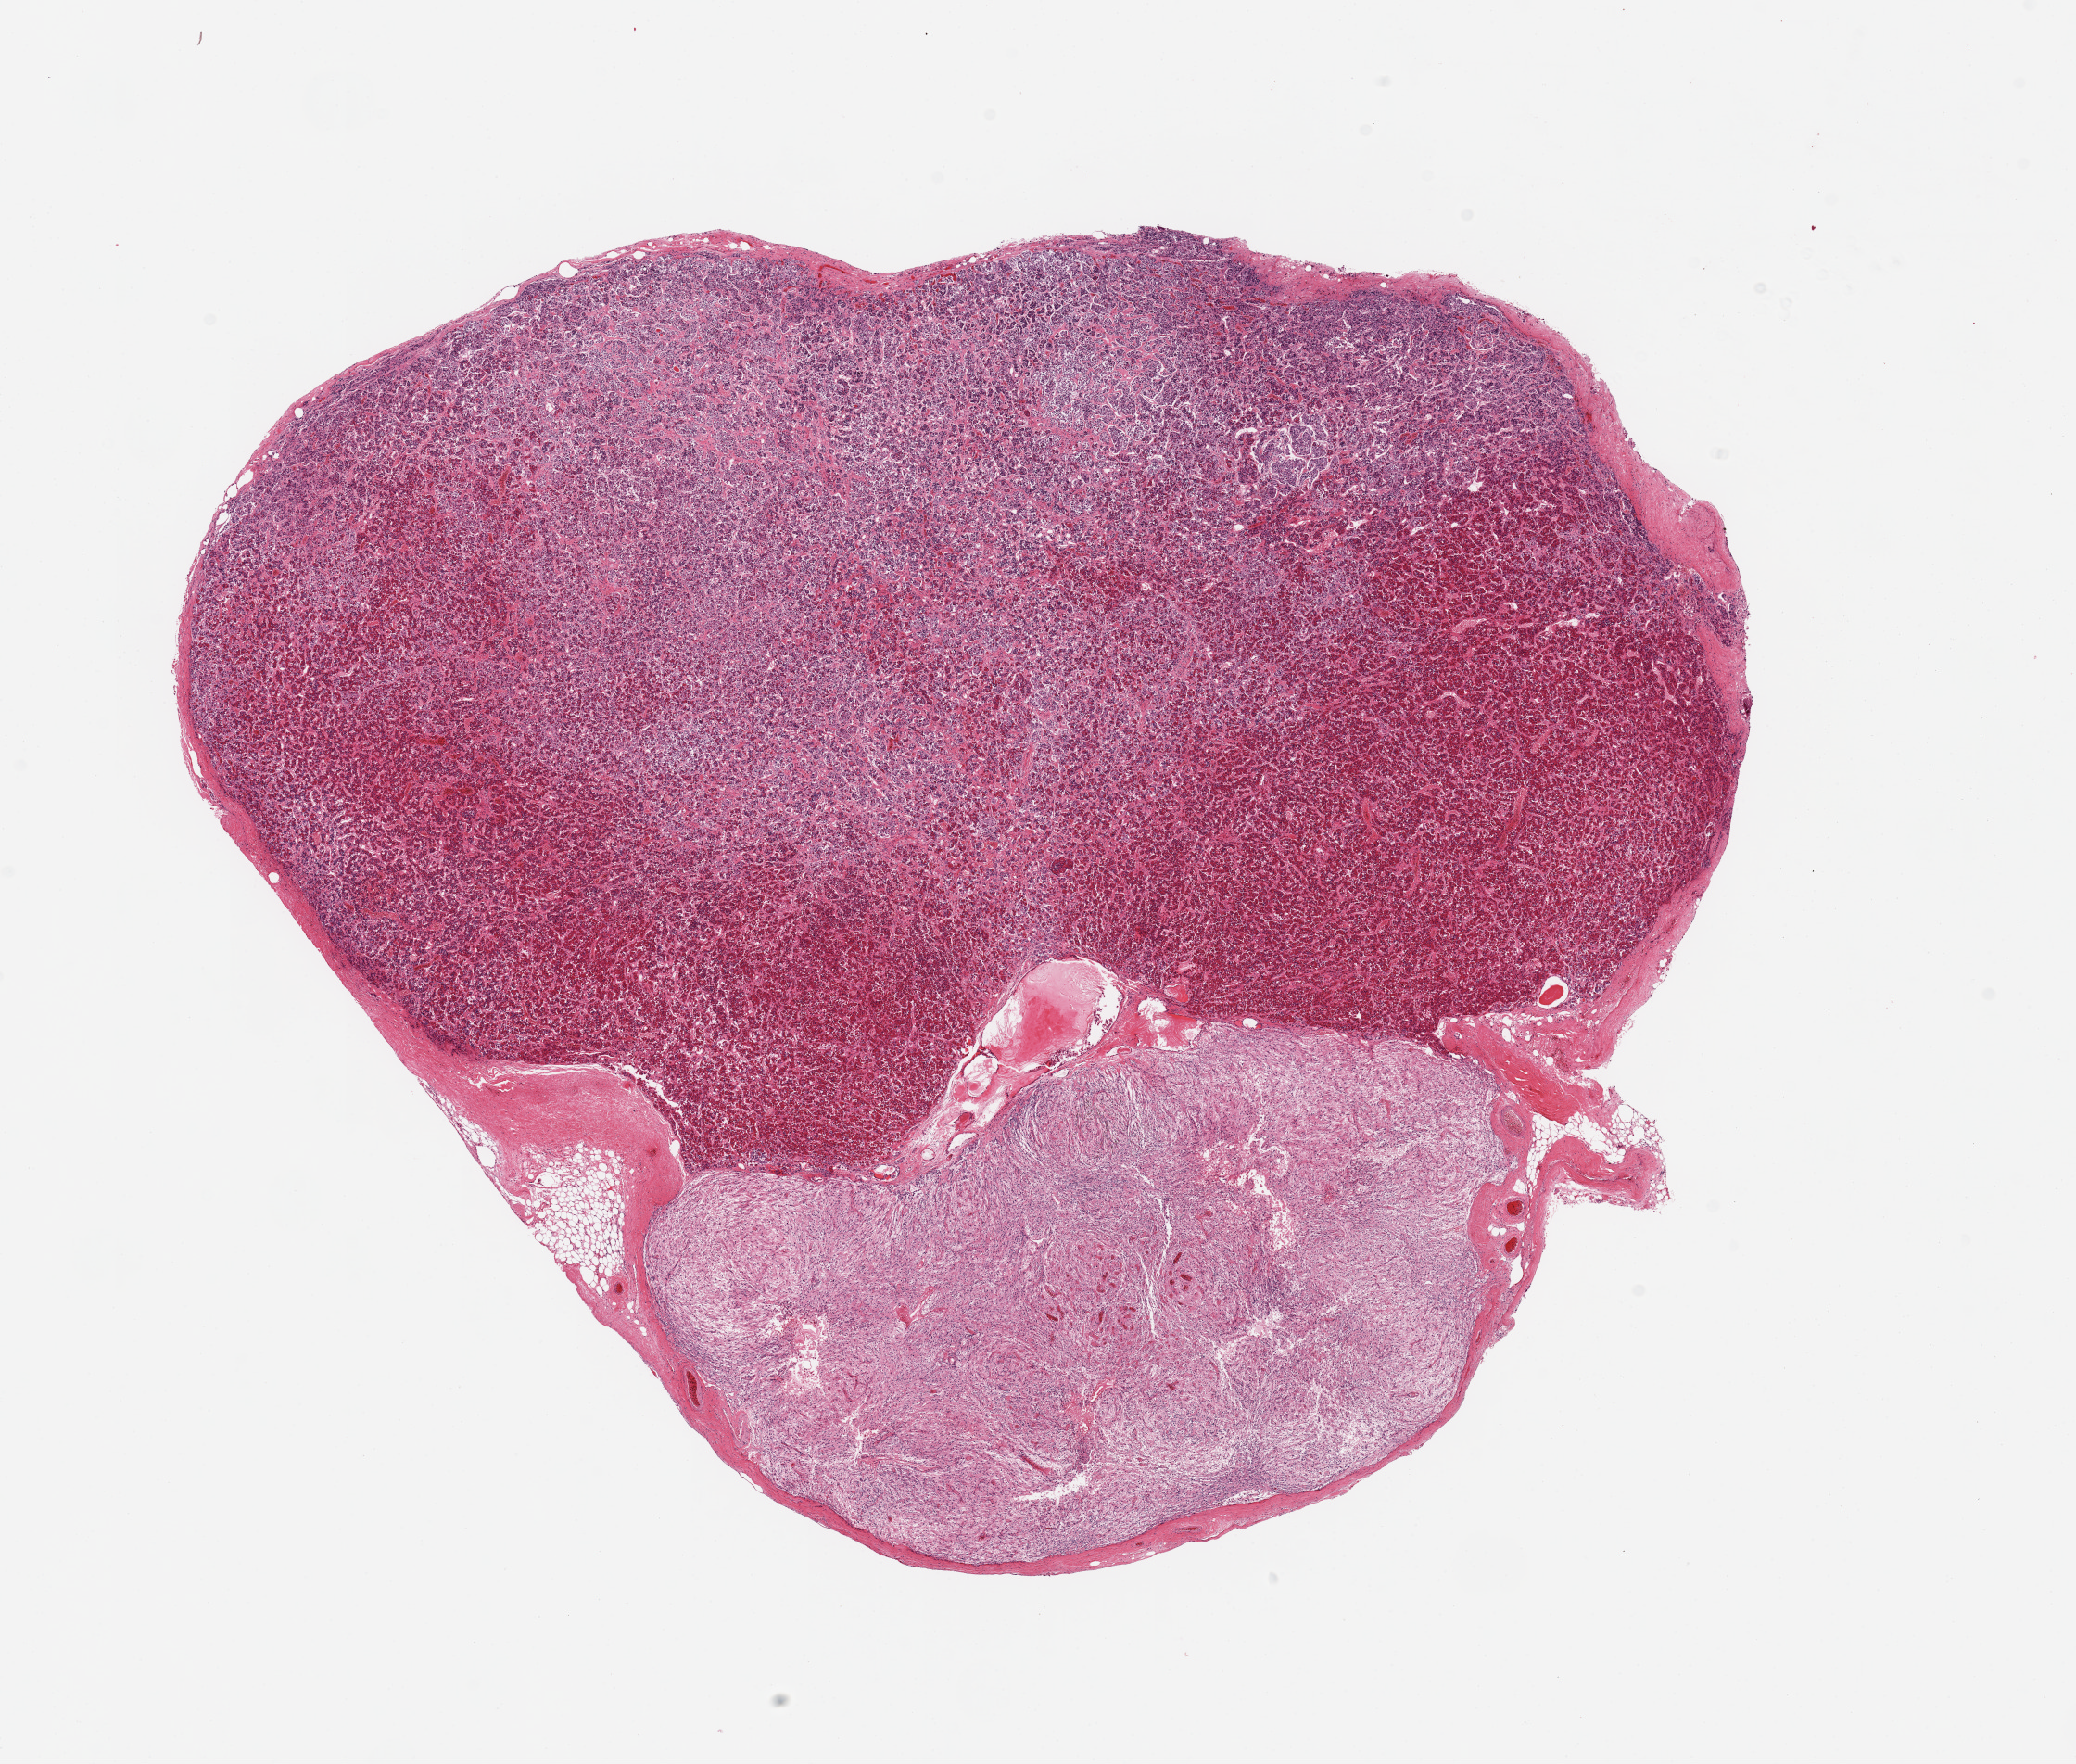
Whole-slide image, hematoxylin and eosin (H&E) stain, brightfield, whole scanned area (about 17.7 x 15.1 mm, slide scanned at 20x) shown as a low-resolution overview, PAXgene-fixed, paraffin-embedded tissue, sampled site (target tissue): pituitary, donor tissue sample. Donor: male.
• review note (as recorded): 1 pieces, mainly adenohypophysis; 7x4mm portion of neurohypophysis